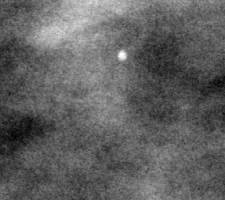
Region of interest cut from a scanned film mammogram (one marked finding), left breast, CC view.
Marked abnormality: calcifications, morphology punctate; BI-RADS assessment category 2; benign without callback (not worked up further).